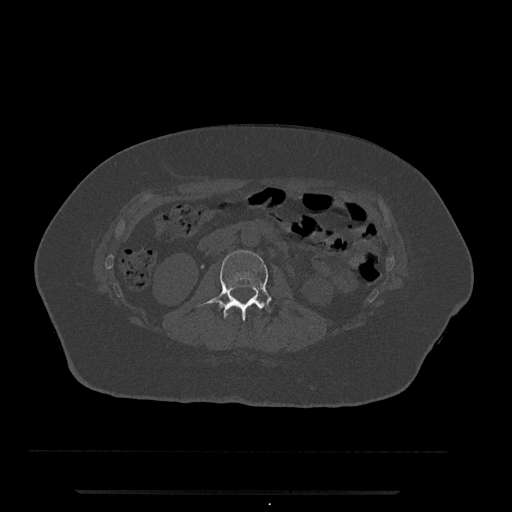
CT including the spine, one axial slice; slice 38 of 797 in the series (ordered by position); reconstruction kernel Br40s/3; 120 kVp; bone window (W 1800 / L 400 HU); 512 × 512 image matrix, field of view 440 × 440 mm. Female patient, age 51 years. From the clinical record (not read from this slice): primary cancer: neuro.
Annotated regions visible in this slice (semi-automatically segmented with operator editing):
- L1 vertebra: bounding box [x1, y1, x2, y2] px = [224, 314, 228, 319]
- L2 vertebra: [196, 250, 272, 321]